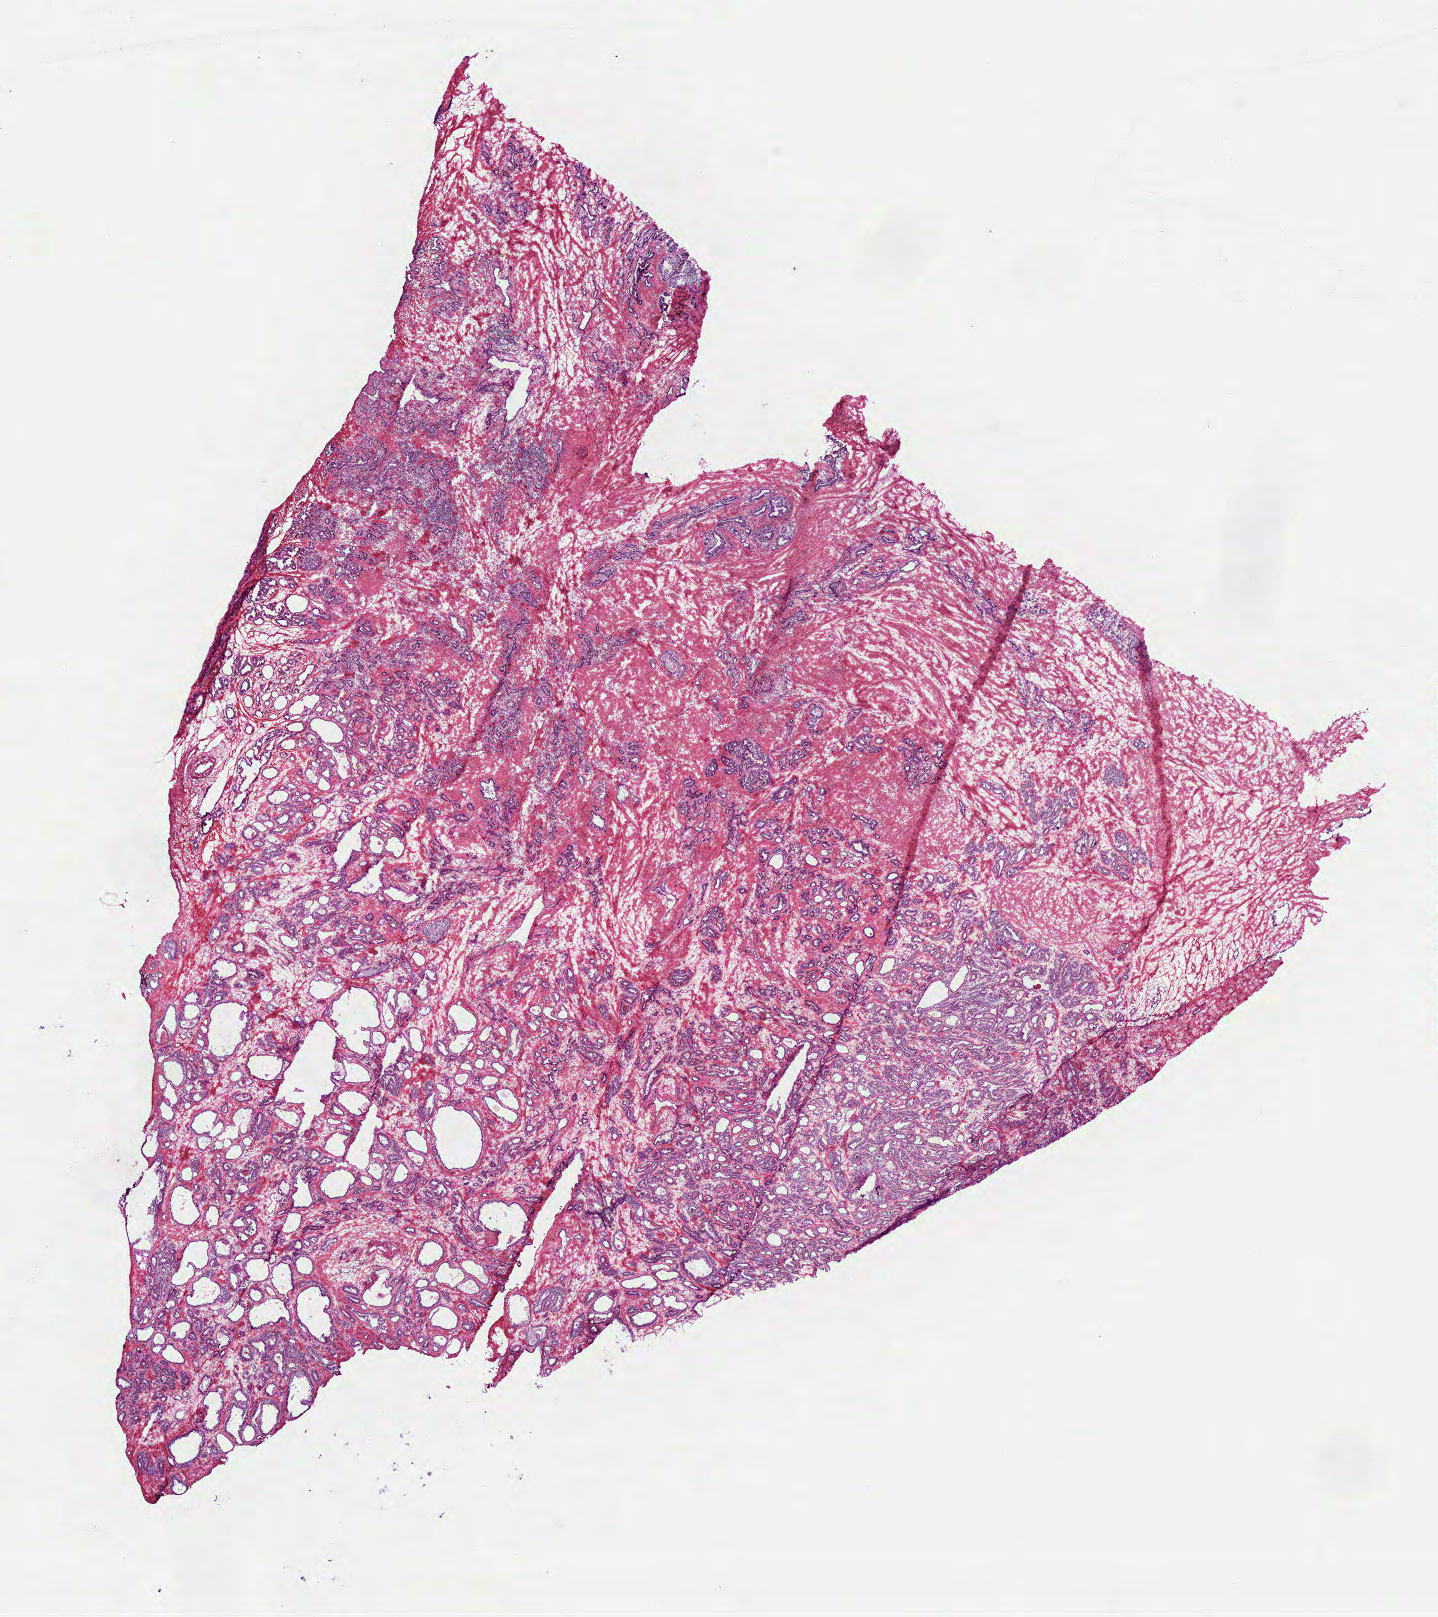
Digitized H&E tissue section (whole slide), low-resolution overview of the scanned area, about 11.6 x 13.0 mm (acquisition: 40x scan); frozen section from the top of the tissue portion; prostate, primary tumour sample. Patient: male, age at initial diagnosis 54 years. Gleason score: 7 (3+4). Composition of this section per pathologist review: tumour cells 60%, tumour nuclei 60%, normal cells 10%, stromal cells 30%, necrosis 0%. Inflammatory infiltration, as recorded: lymphocyte infiltration 0%, monocyte infiltration 0%, neutrophil infiltration 0%.
• lymph nodes positive (case pathology): 0 of 7 examined
• histologic diagnosis: Acinar cell carcinoma (prostate gland)
• laterality: bilateral